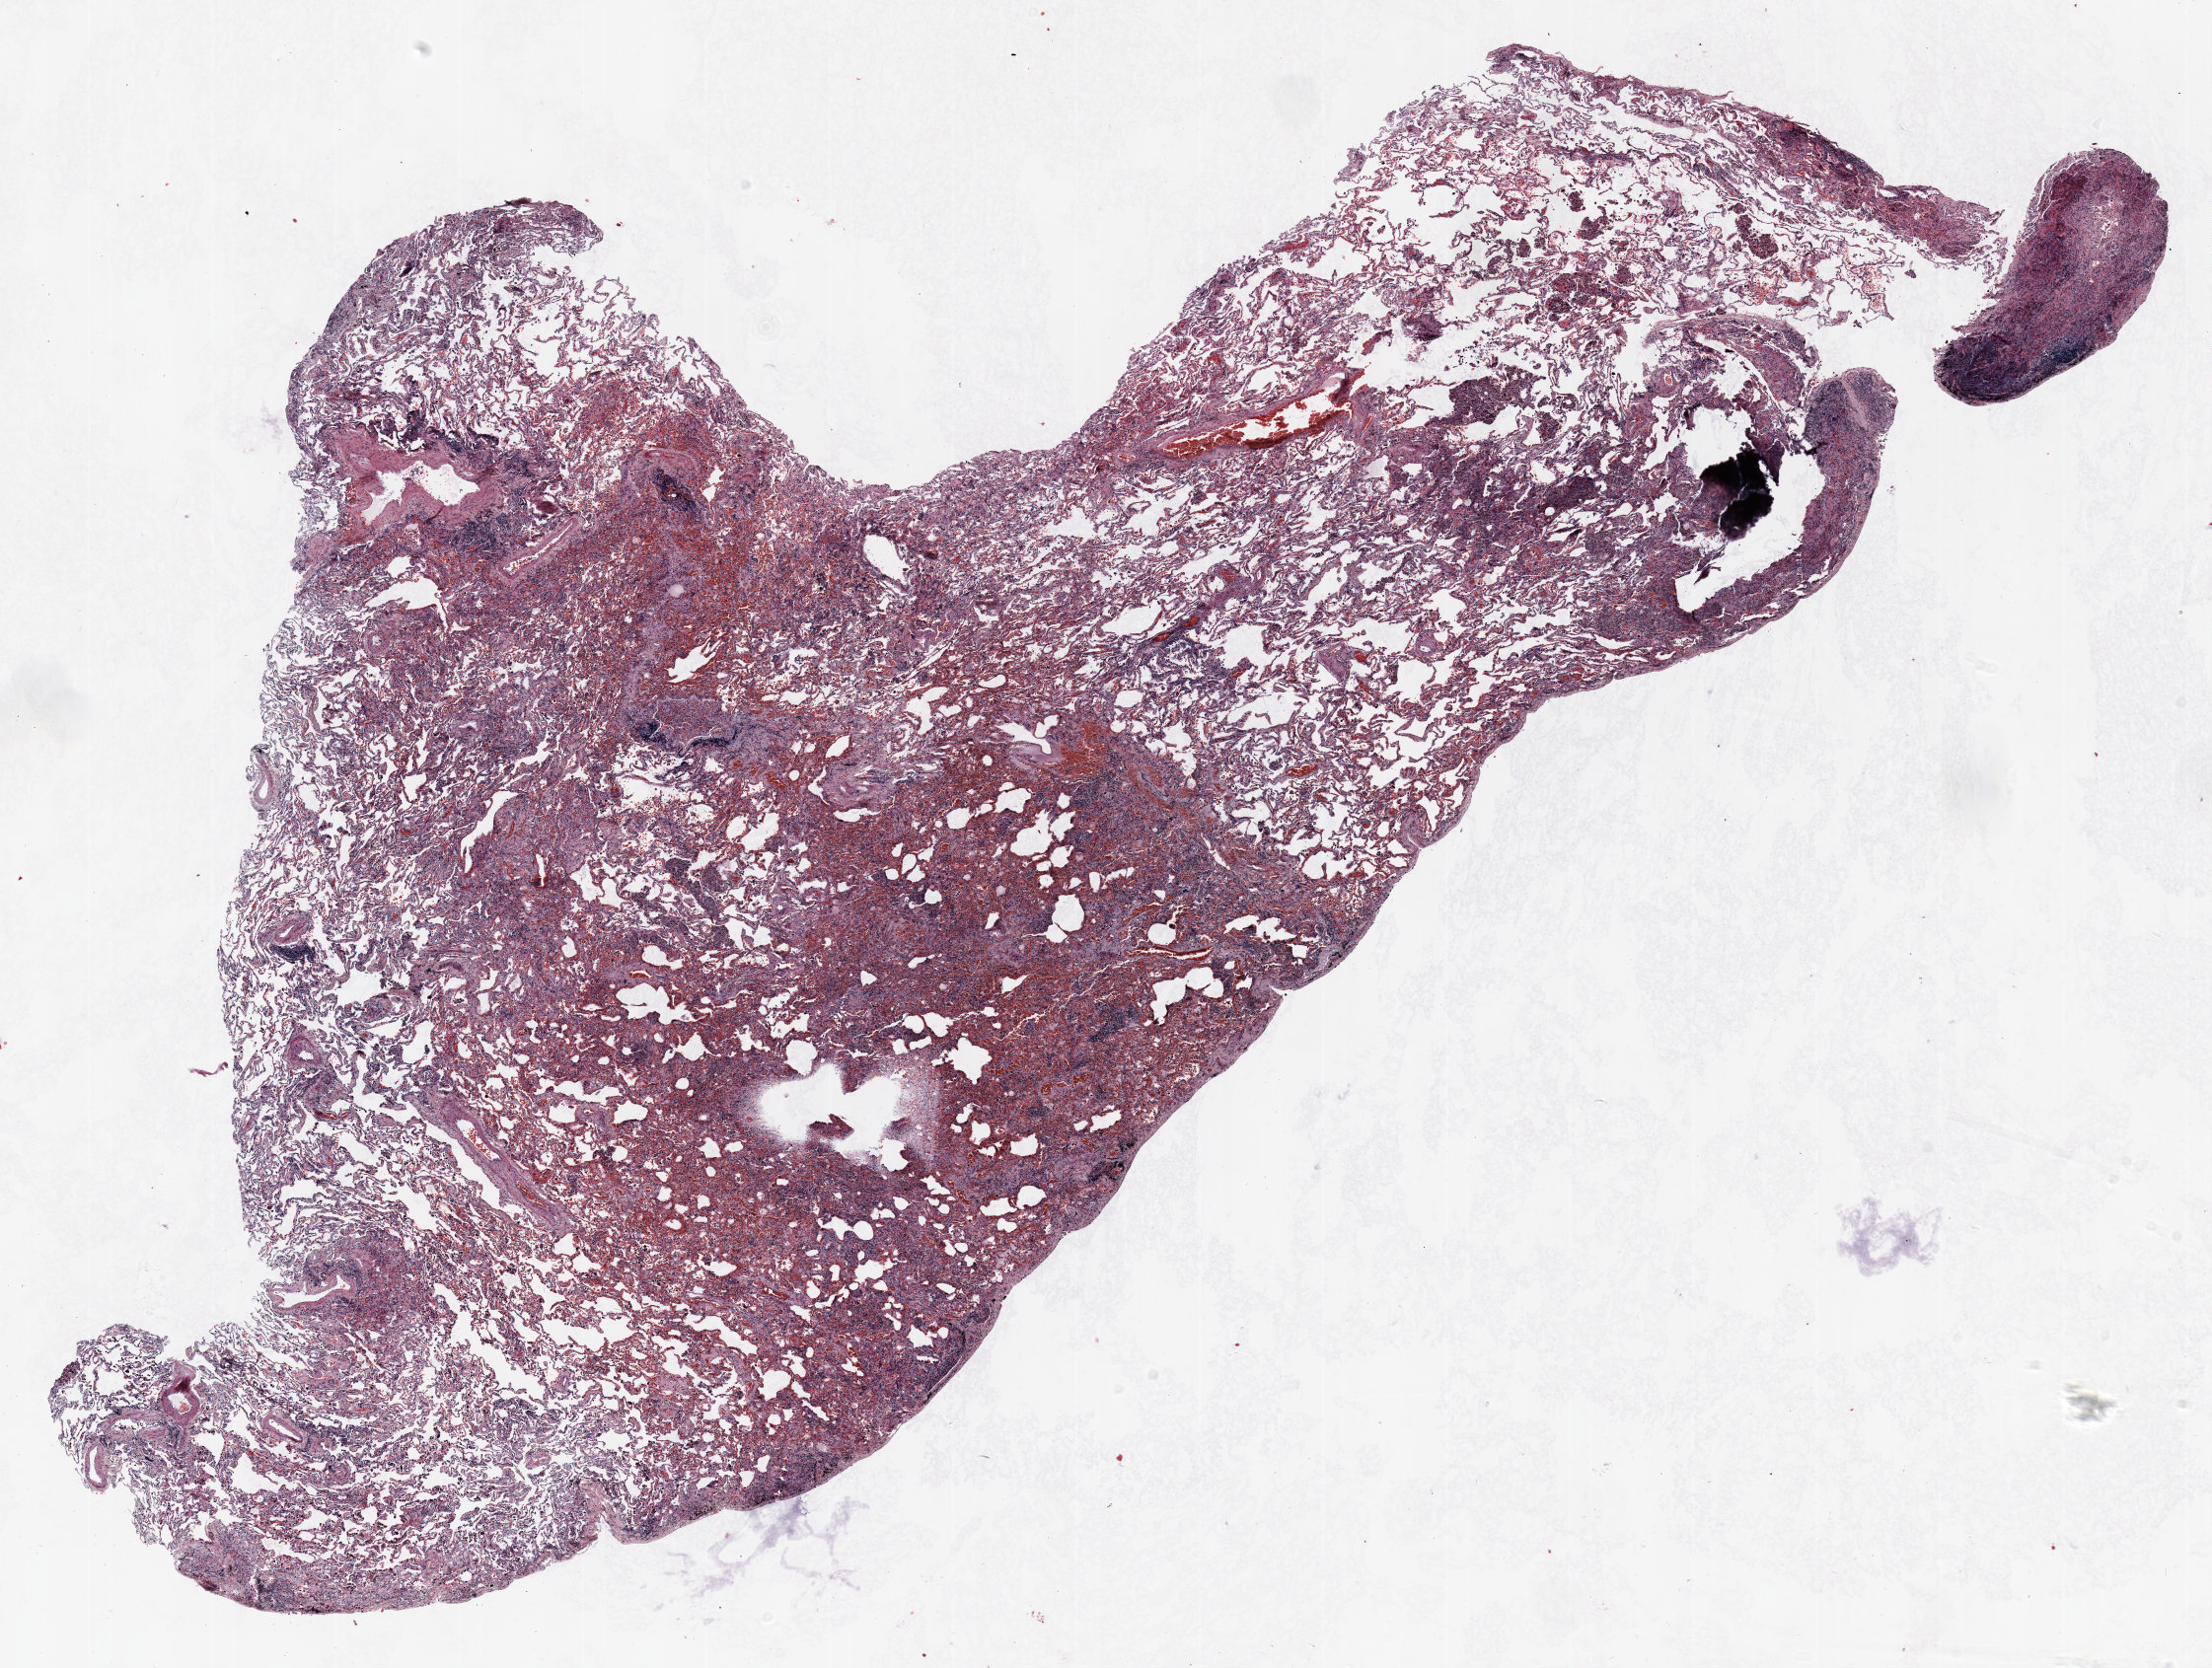
Whole-slide histology image, H&E-stained, shown as a low-resolution overview of the whole scanned area (about 18.0 x 13.6 mm, acquisition: 20x scan), FFPE section, lung. Male, age 55 at enrolment. Current smoker at enrolment. Grade: moderately differentiated (G2).
Primary tumour location (clinical record): left upper lobe. ICD-O-3 topography: upper lobe of lung (C34.1). Participant's lung-cancer diagnosis: Adenocarcinoma, NOS (ICD-O-3 8140/3). Tumour size (pathology): 8 mm. Stage (AJCC 6th edition): IA.